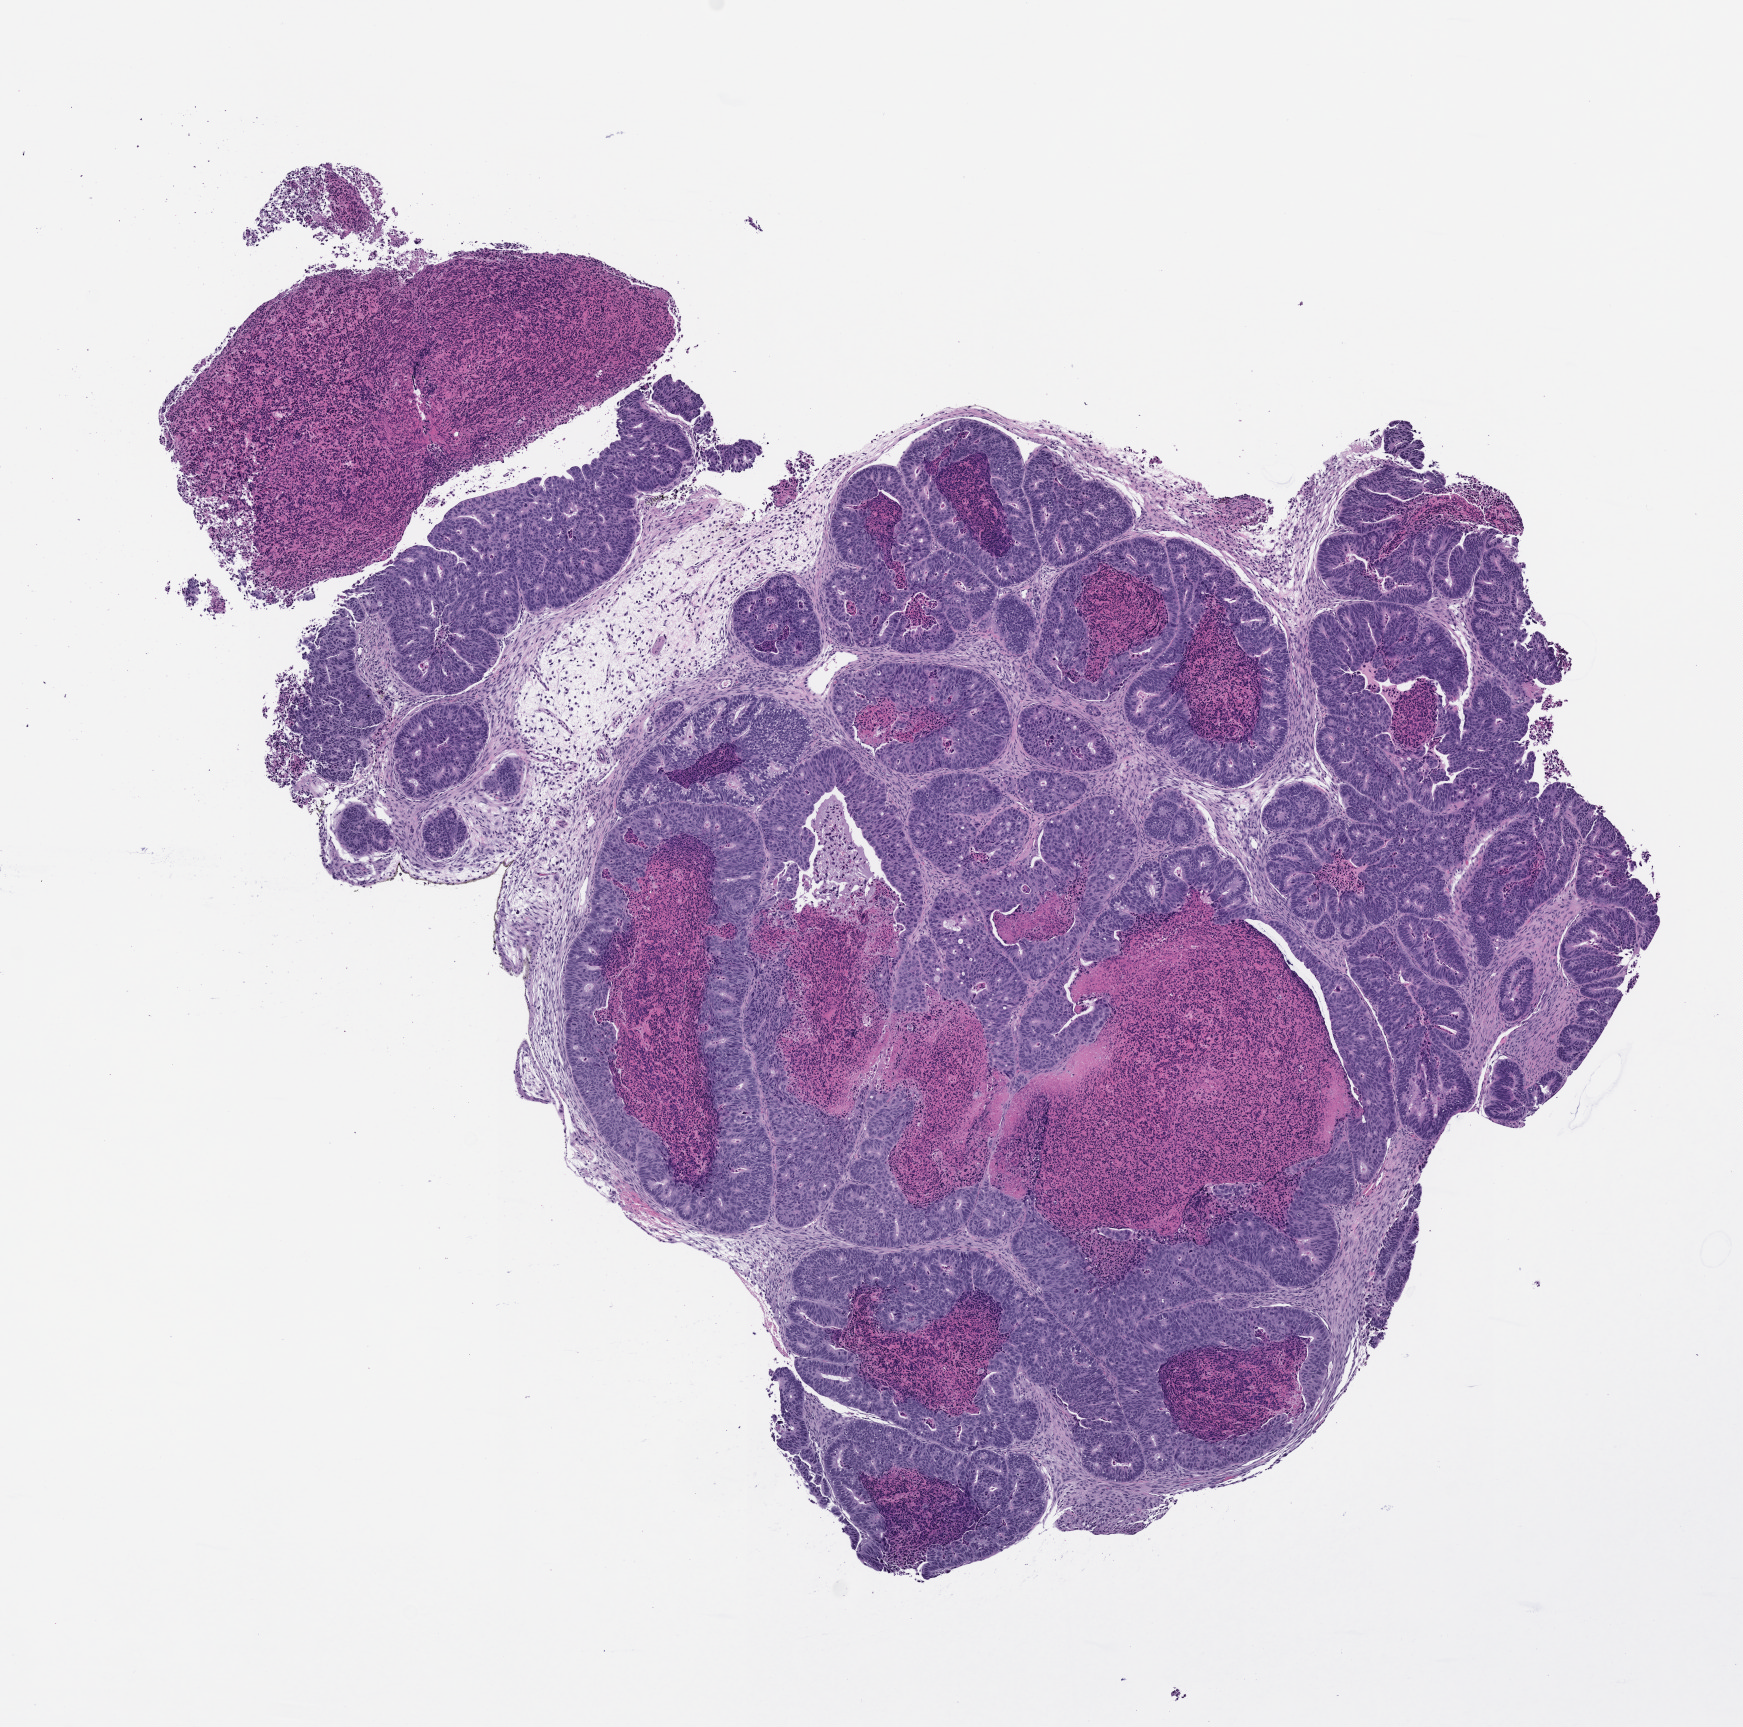
H&E whole-slide image of a patient-derived xenograft (PDX) tumor grown in a mouse, passage 1 — whole scanned area (about 7.0 x 6.9 mm) shown as a low-resolution overview, formalin-fixed, paraffin-embedded (FFPE) tissue, tumor site category: colon.
Originating patient diagnosis: Colon Adenocarcinoma.